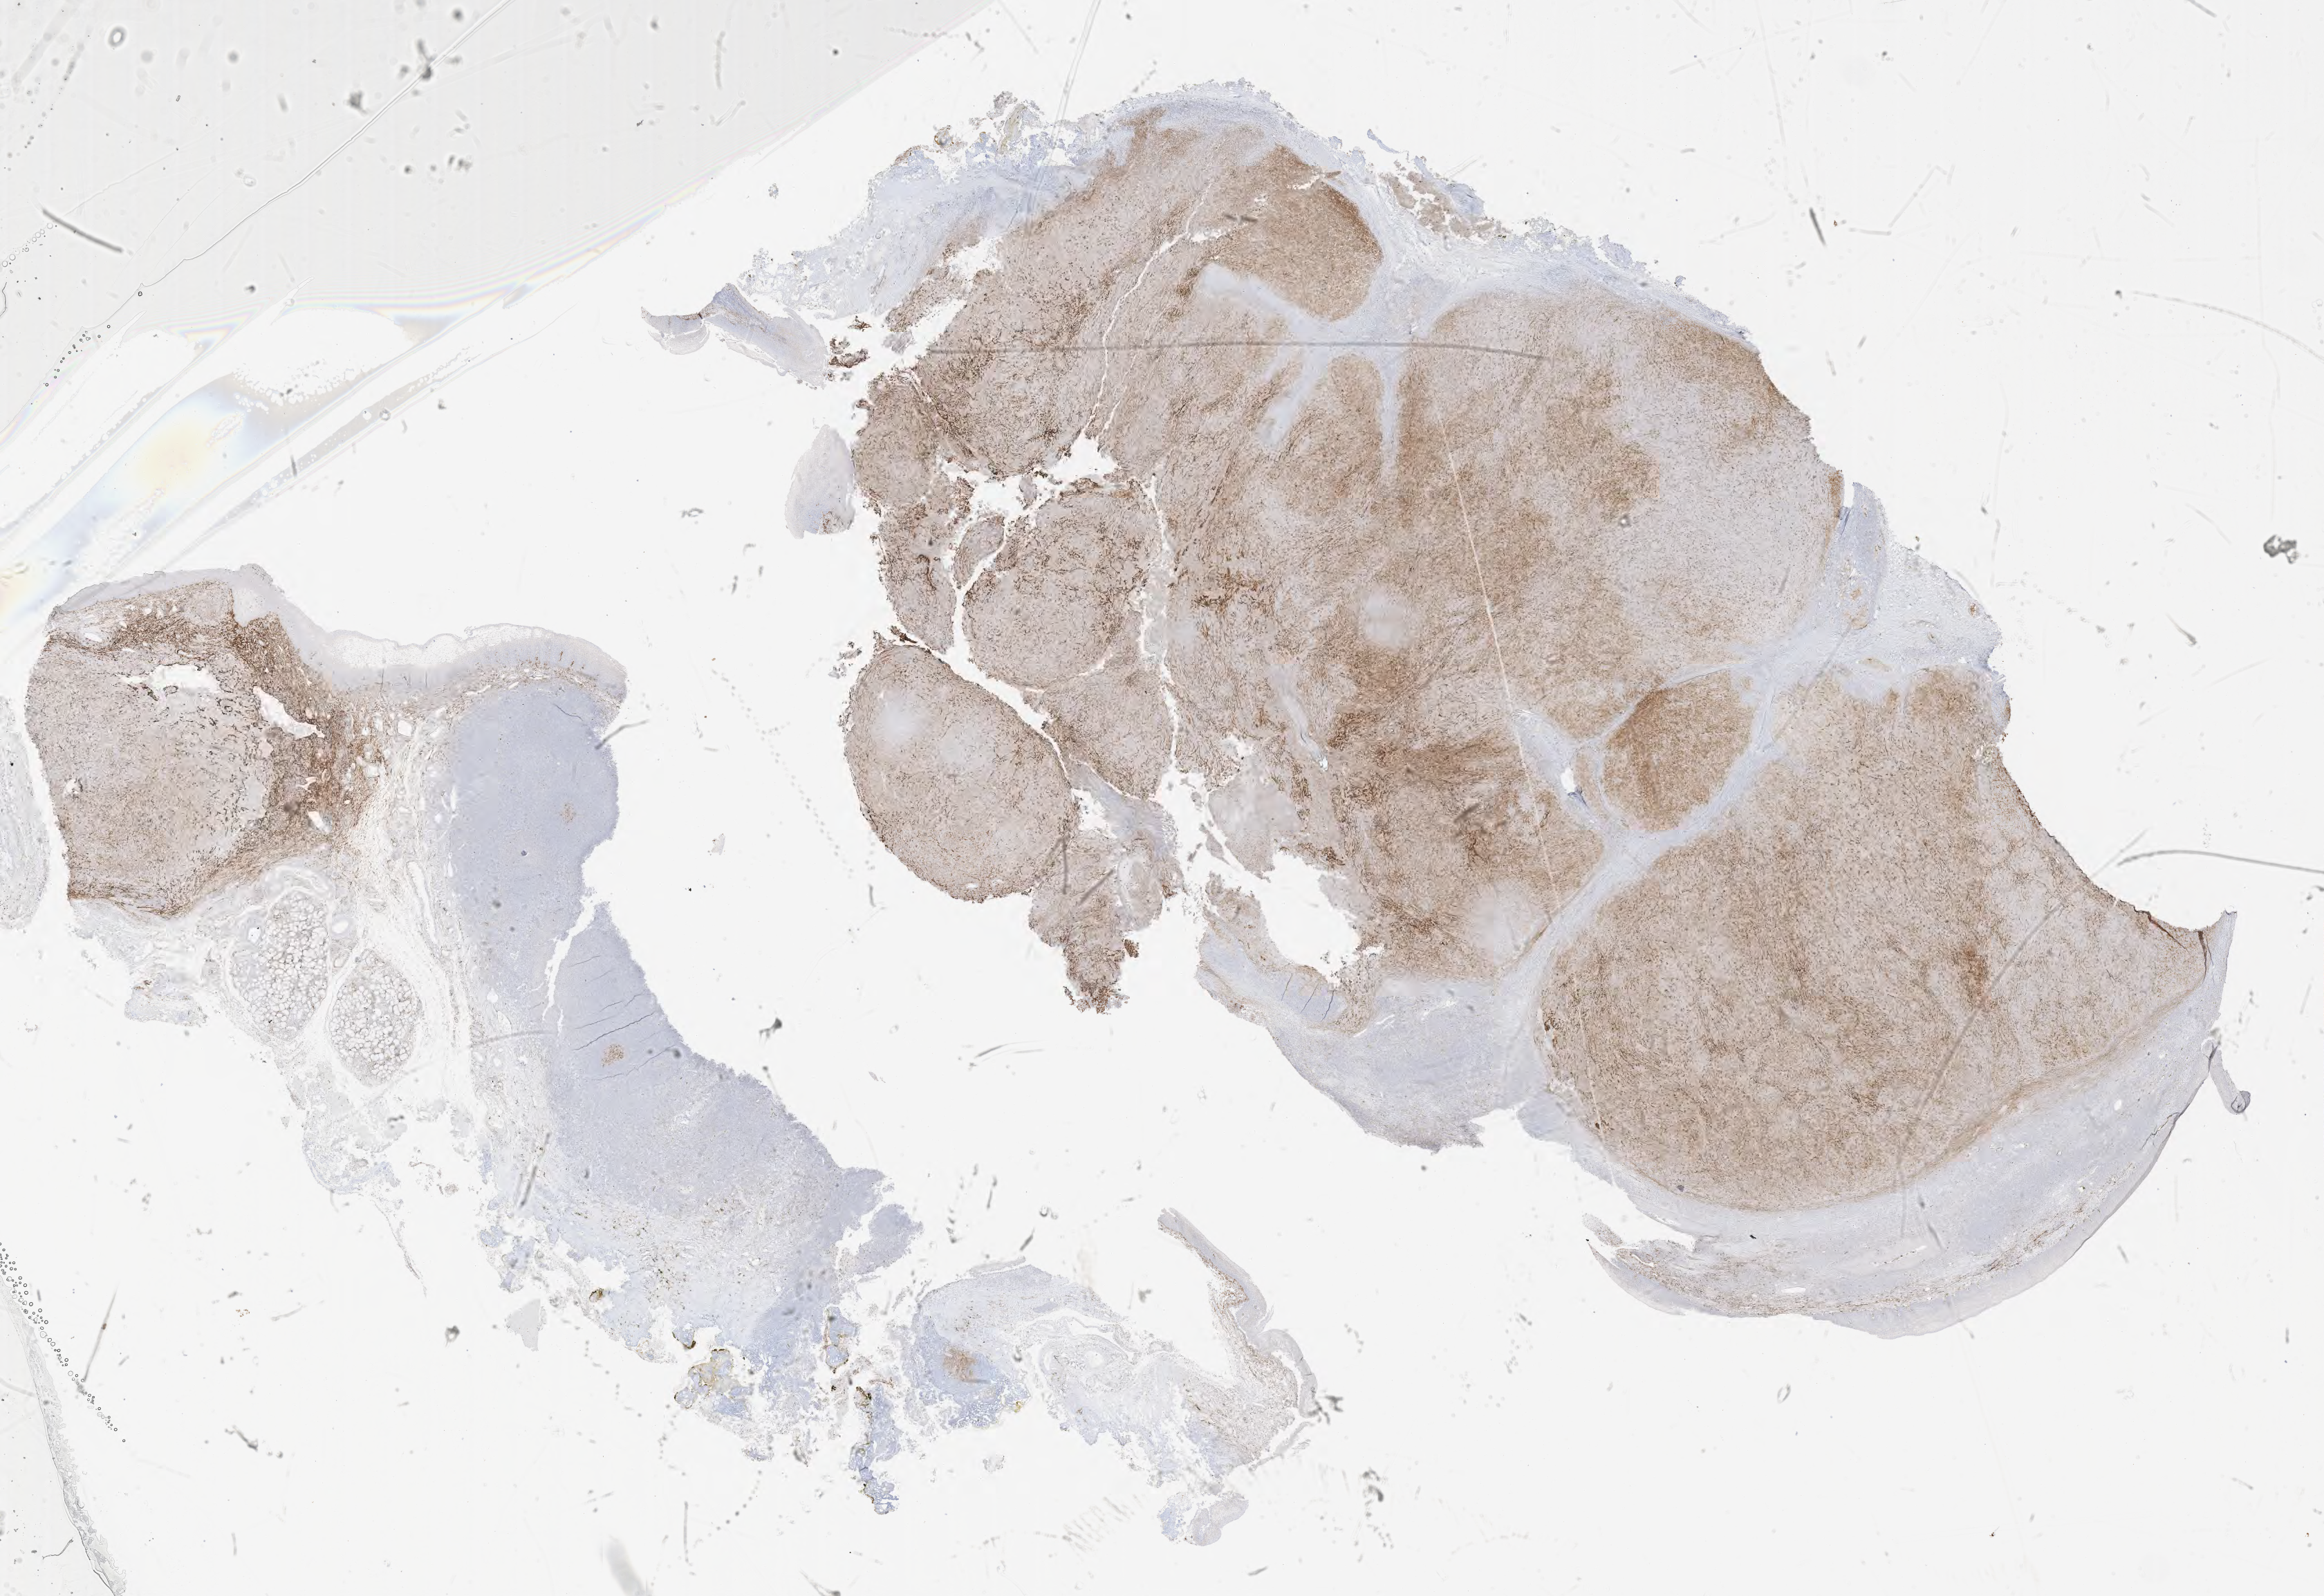
Immunohistochemistry (IHC) whole-slide image stained for CD10 — low-resolution overview of the scanned area, about 27.2 x 18.7 mm. Specimen: tumor tissue. Anatomic site: lymph node. Patient: male, aged 56.
Diagnosis: Diffuse large B-cell lymphoma, NOS.